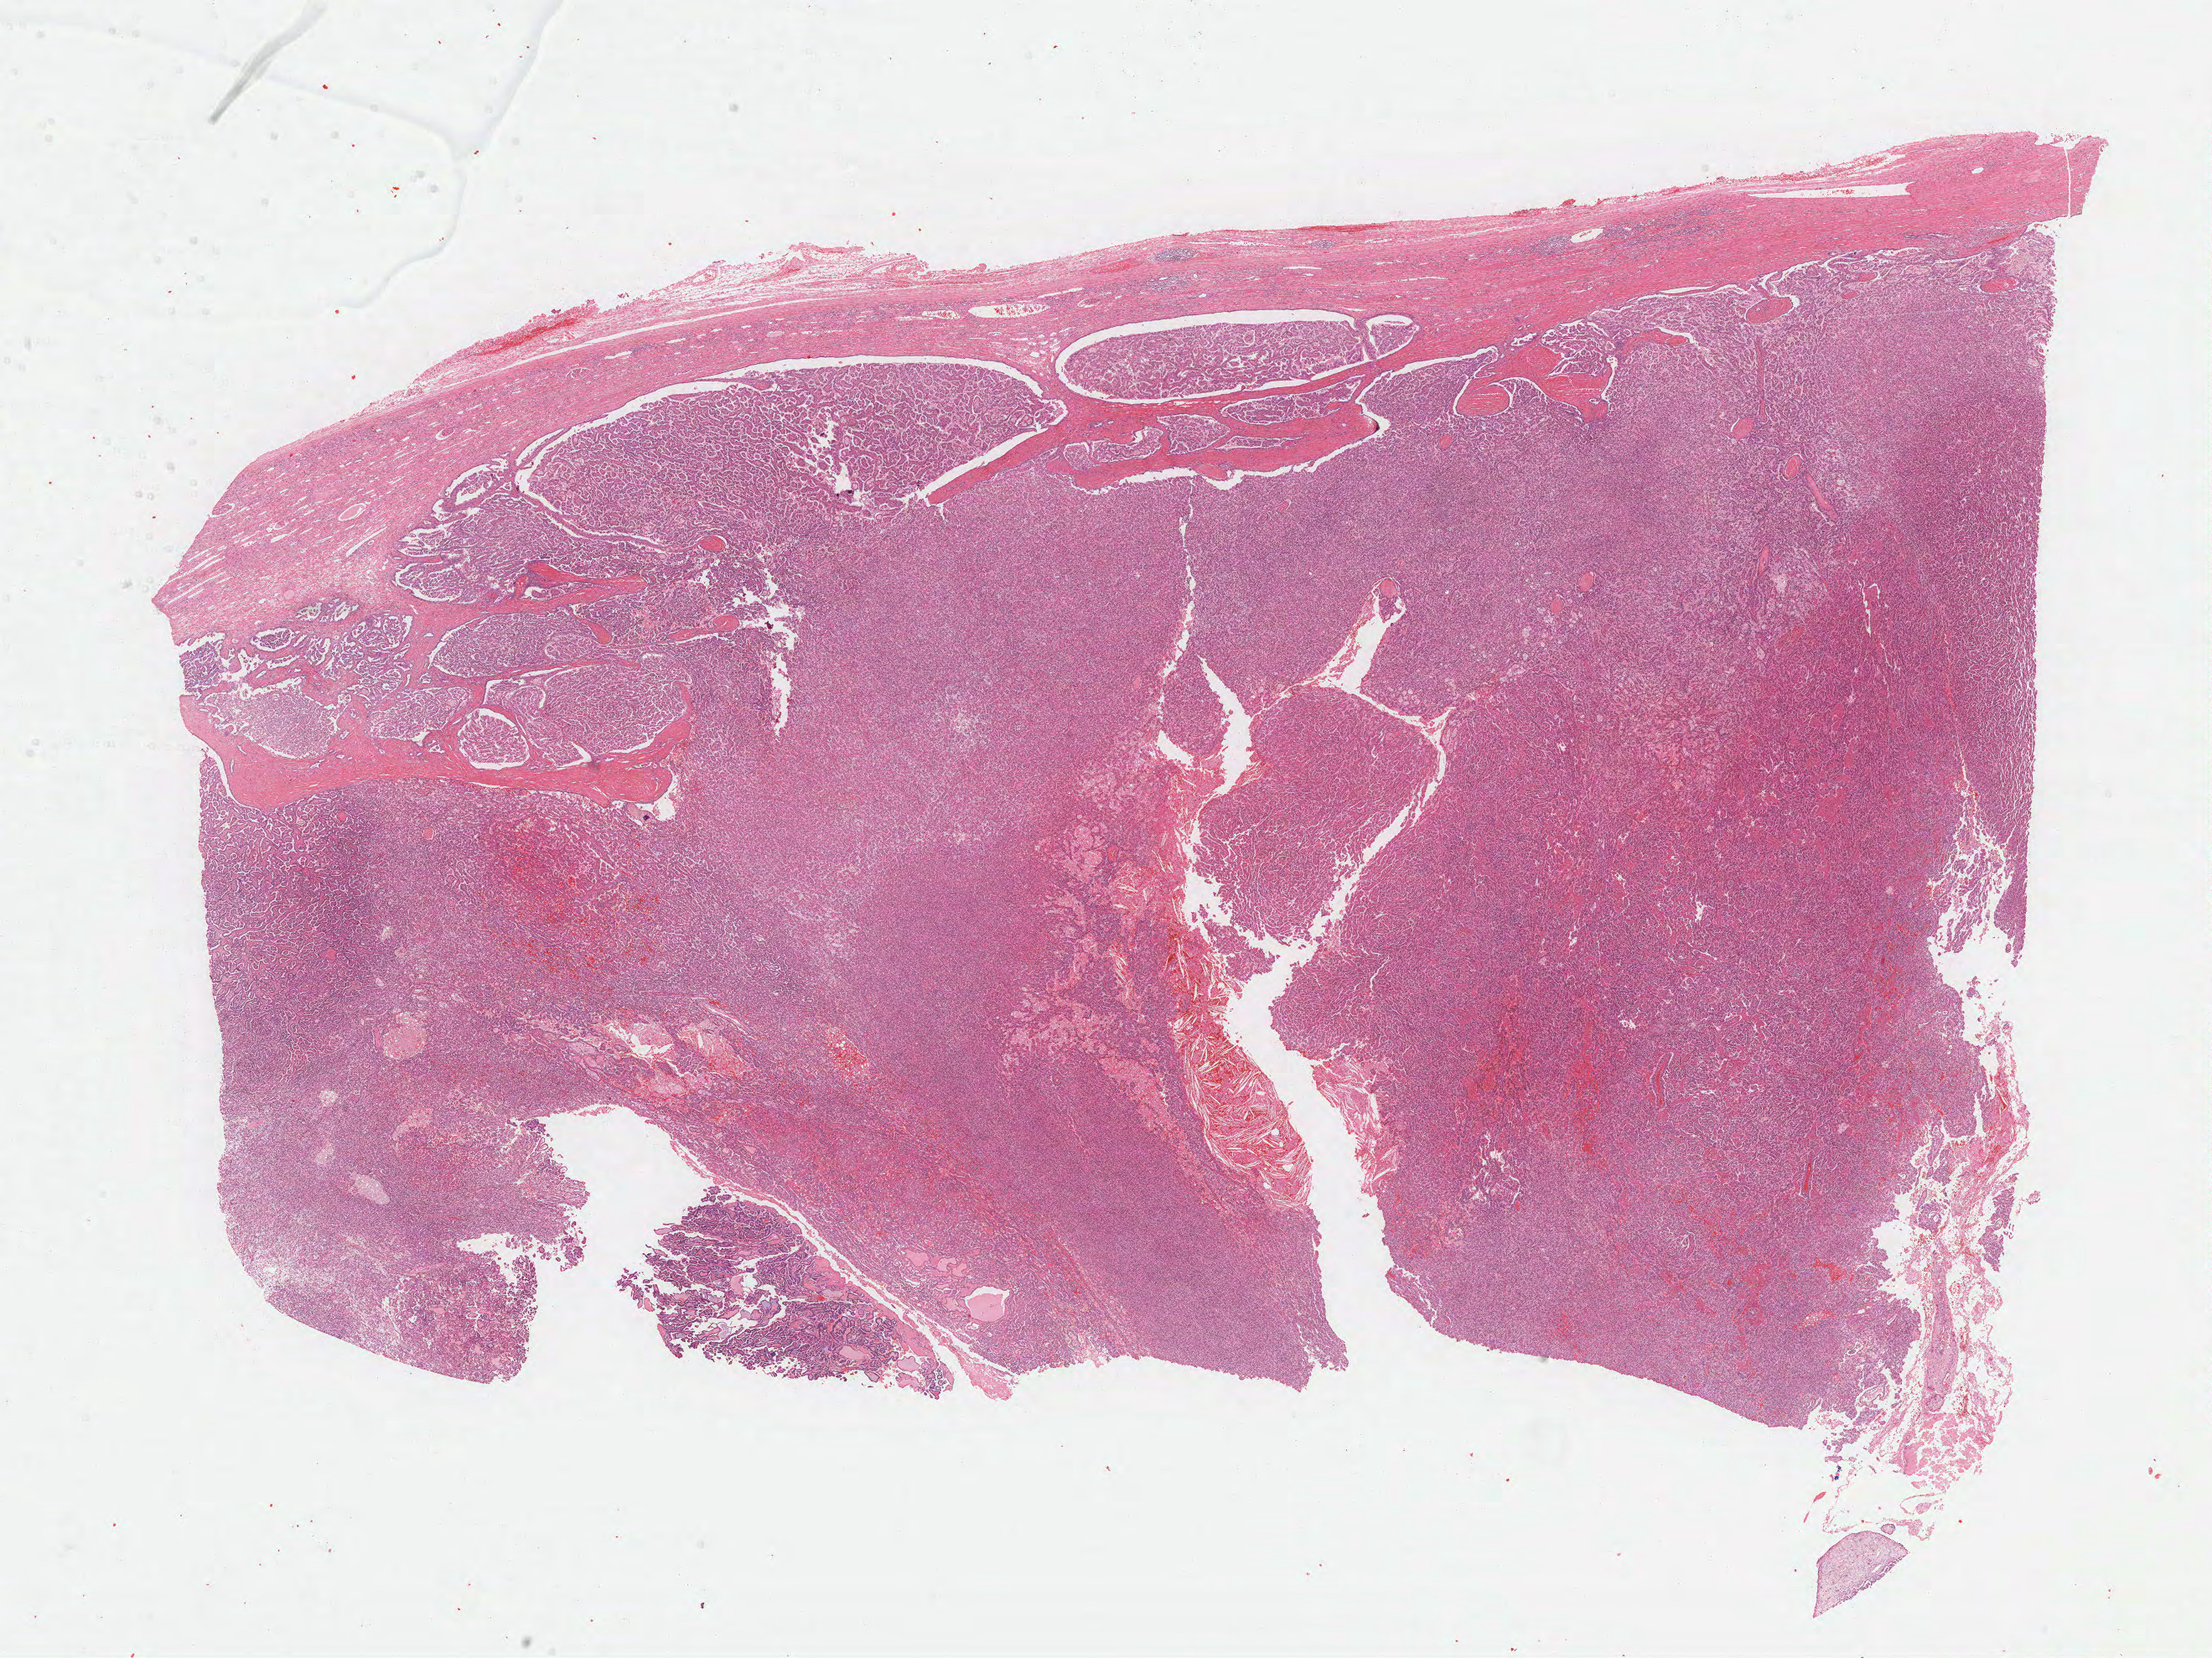
Digitized H&E tissue section (whole slide) — whole scanned area (about 21.3 x 16.0 mm) shown as a low-resolution overview; FFPE section; sample: primary tumour, kidney. Male, age 63 years at initial diagnosis.
Histologic diagnosis: Papillary adenocarcinoma, NOS. AJCC pathologic stage: IV.